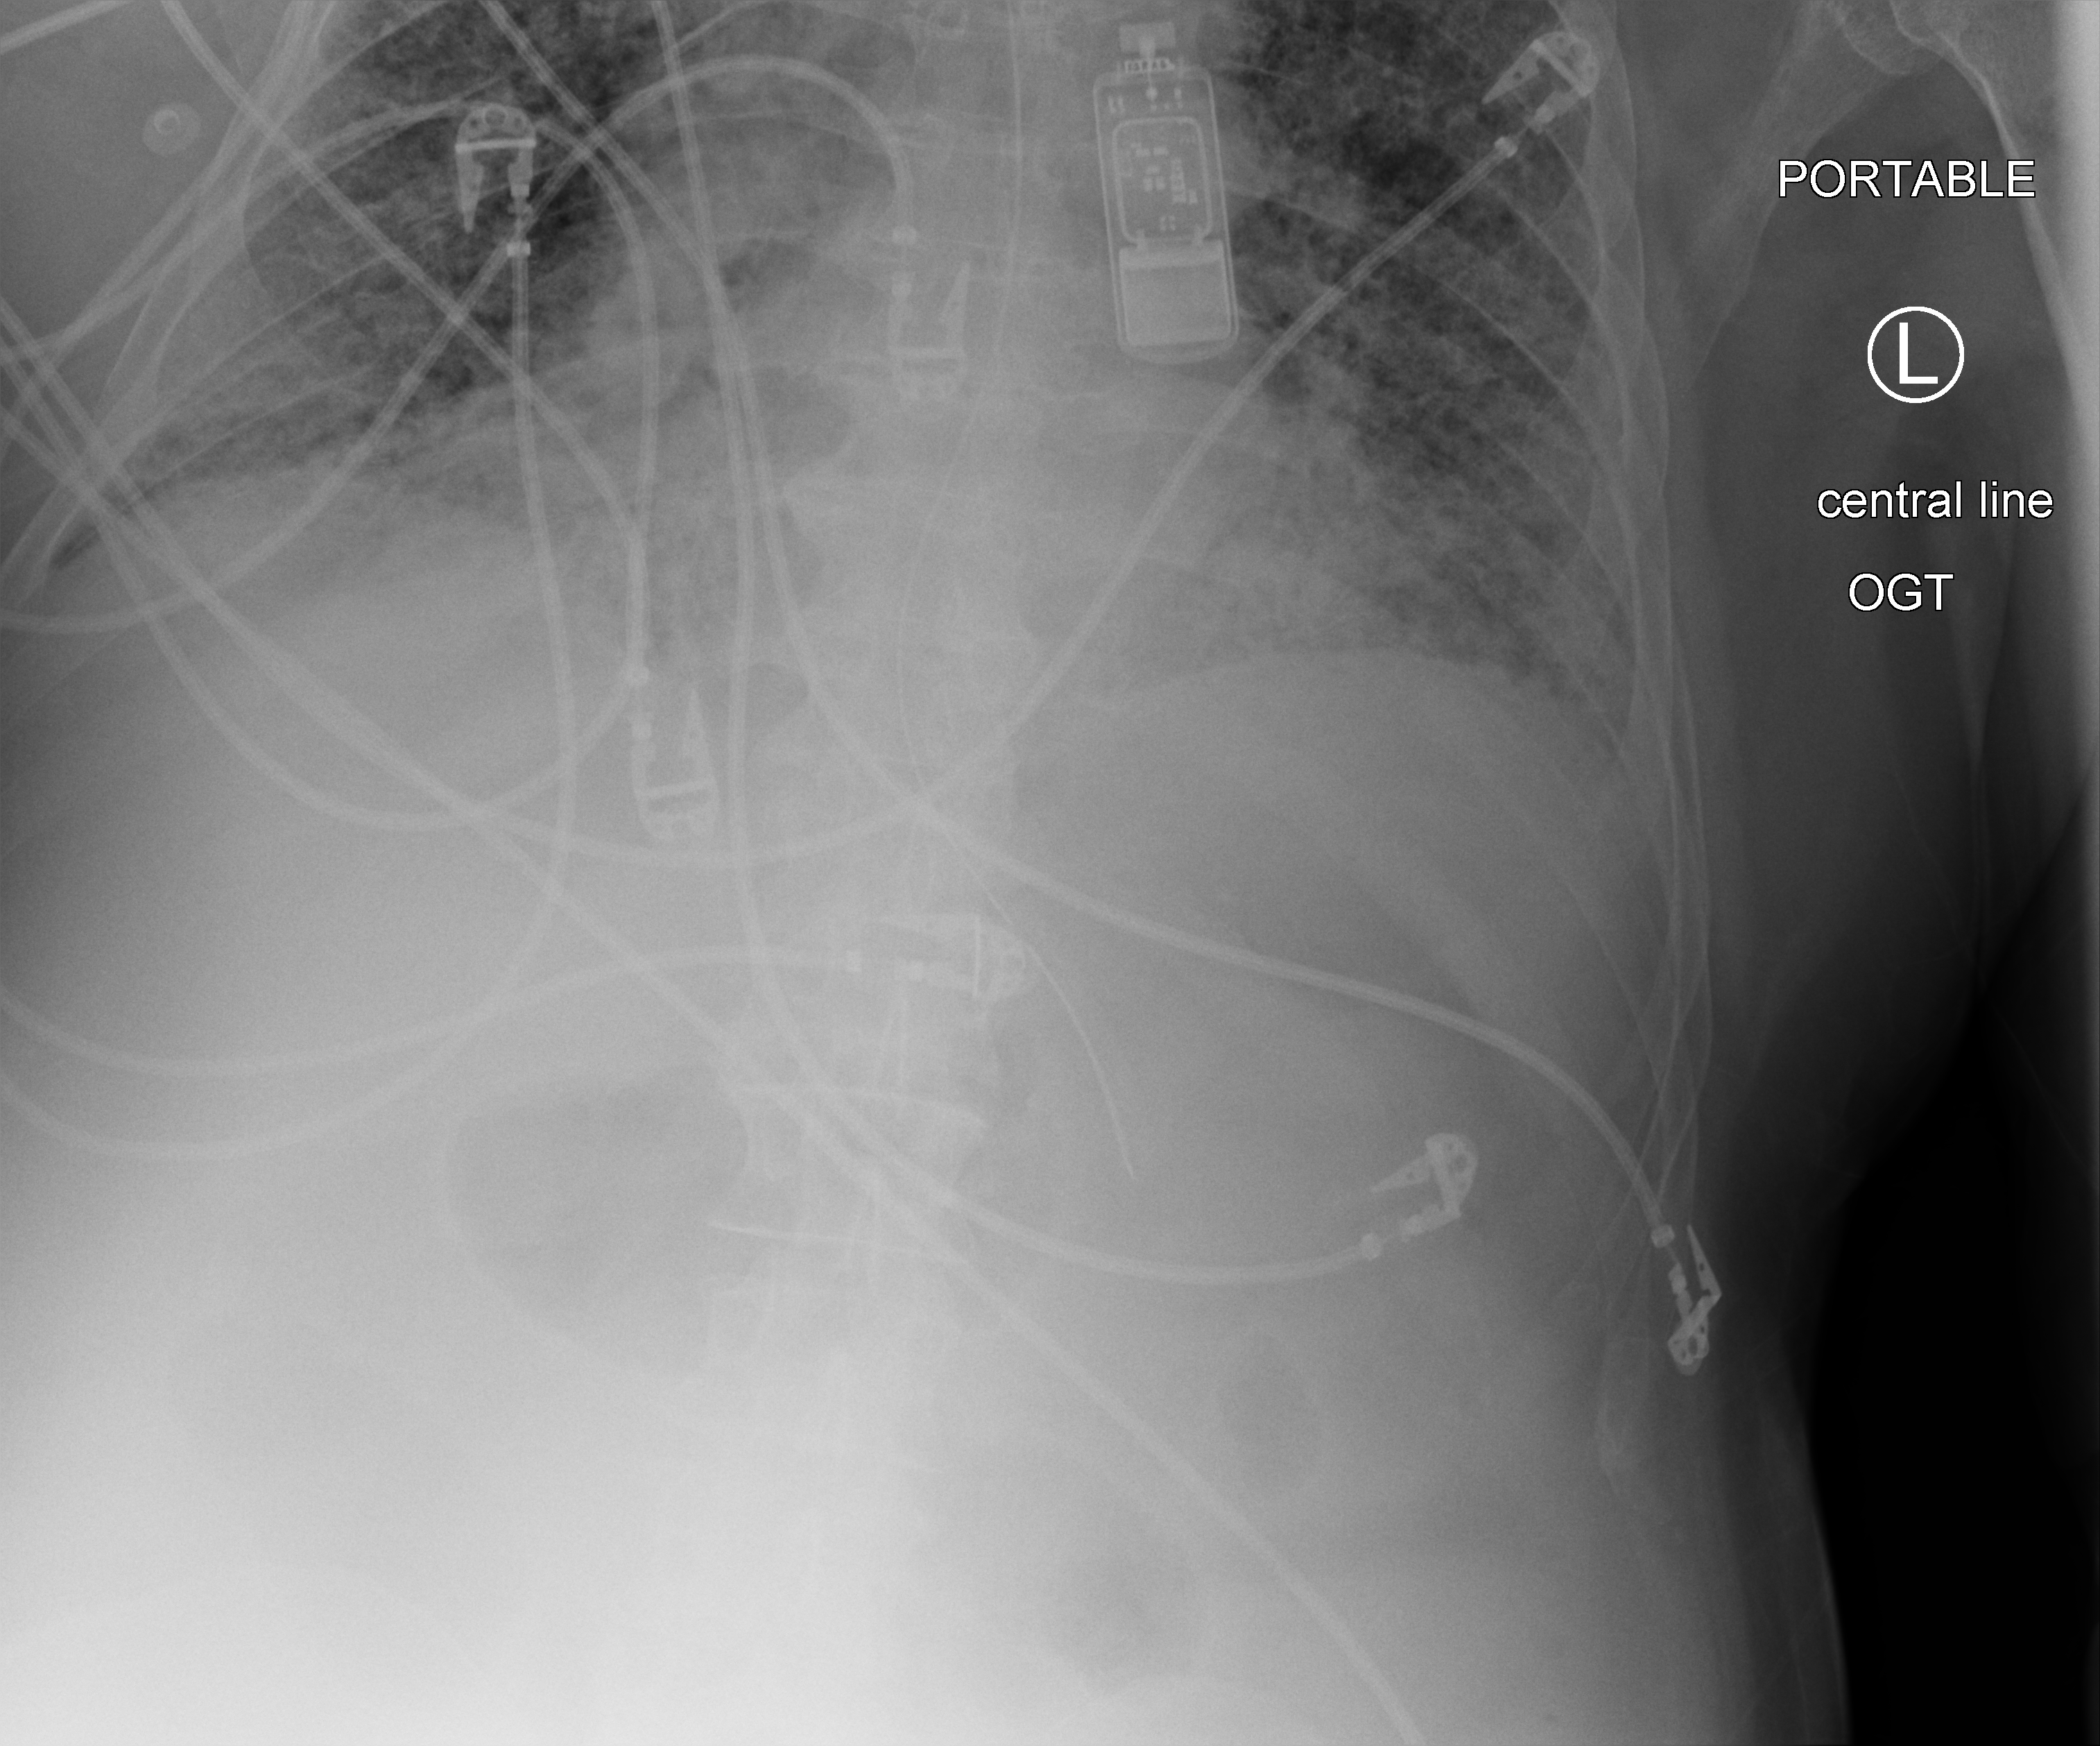
Bedside chest radiograph (computed radiography); anteroposterior (AP) projection. Patient hospitalised with COVID-19; male, aged 60–74 years.
From the hospital-stay record, not from the radiograph (when in the stay this image was taken is not recorded): mechanically ventilated during this hospital stay: yes; other chronic lung disease (admission record): yes; hypertension (admission record): yes.